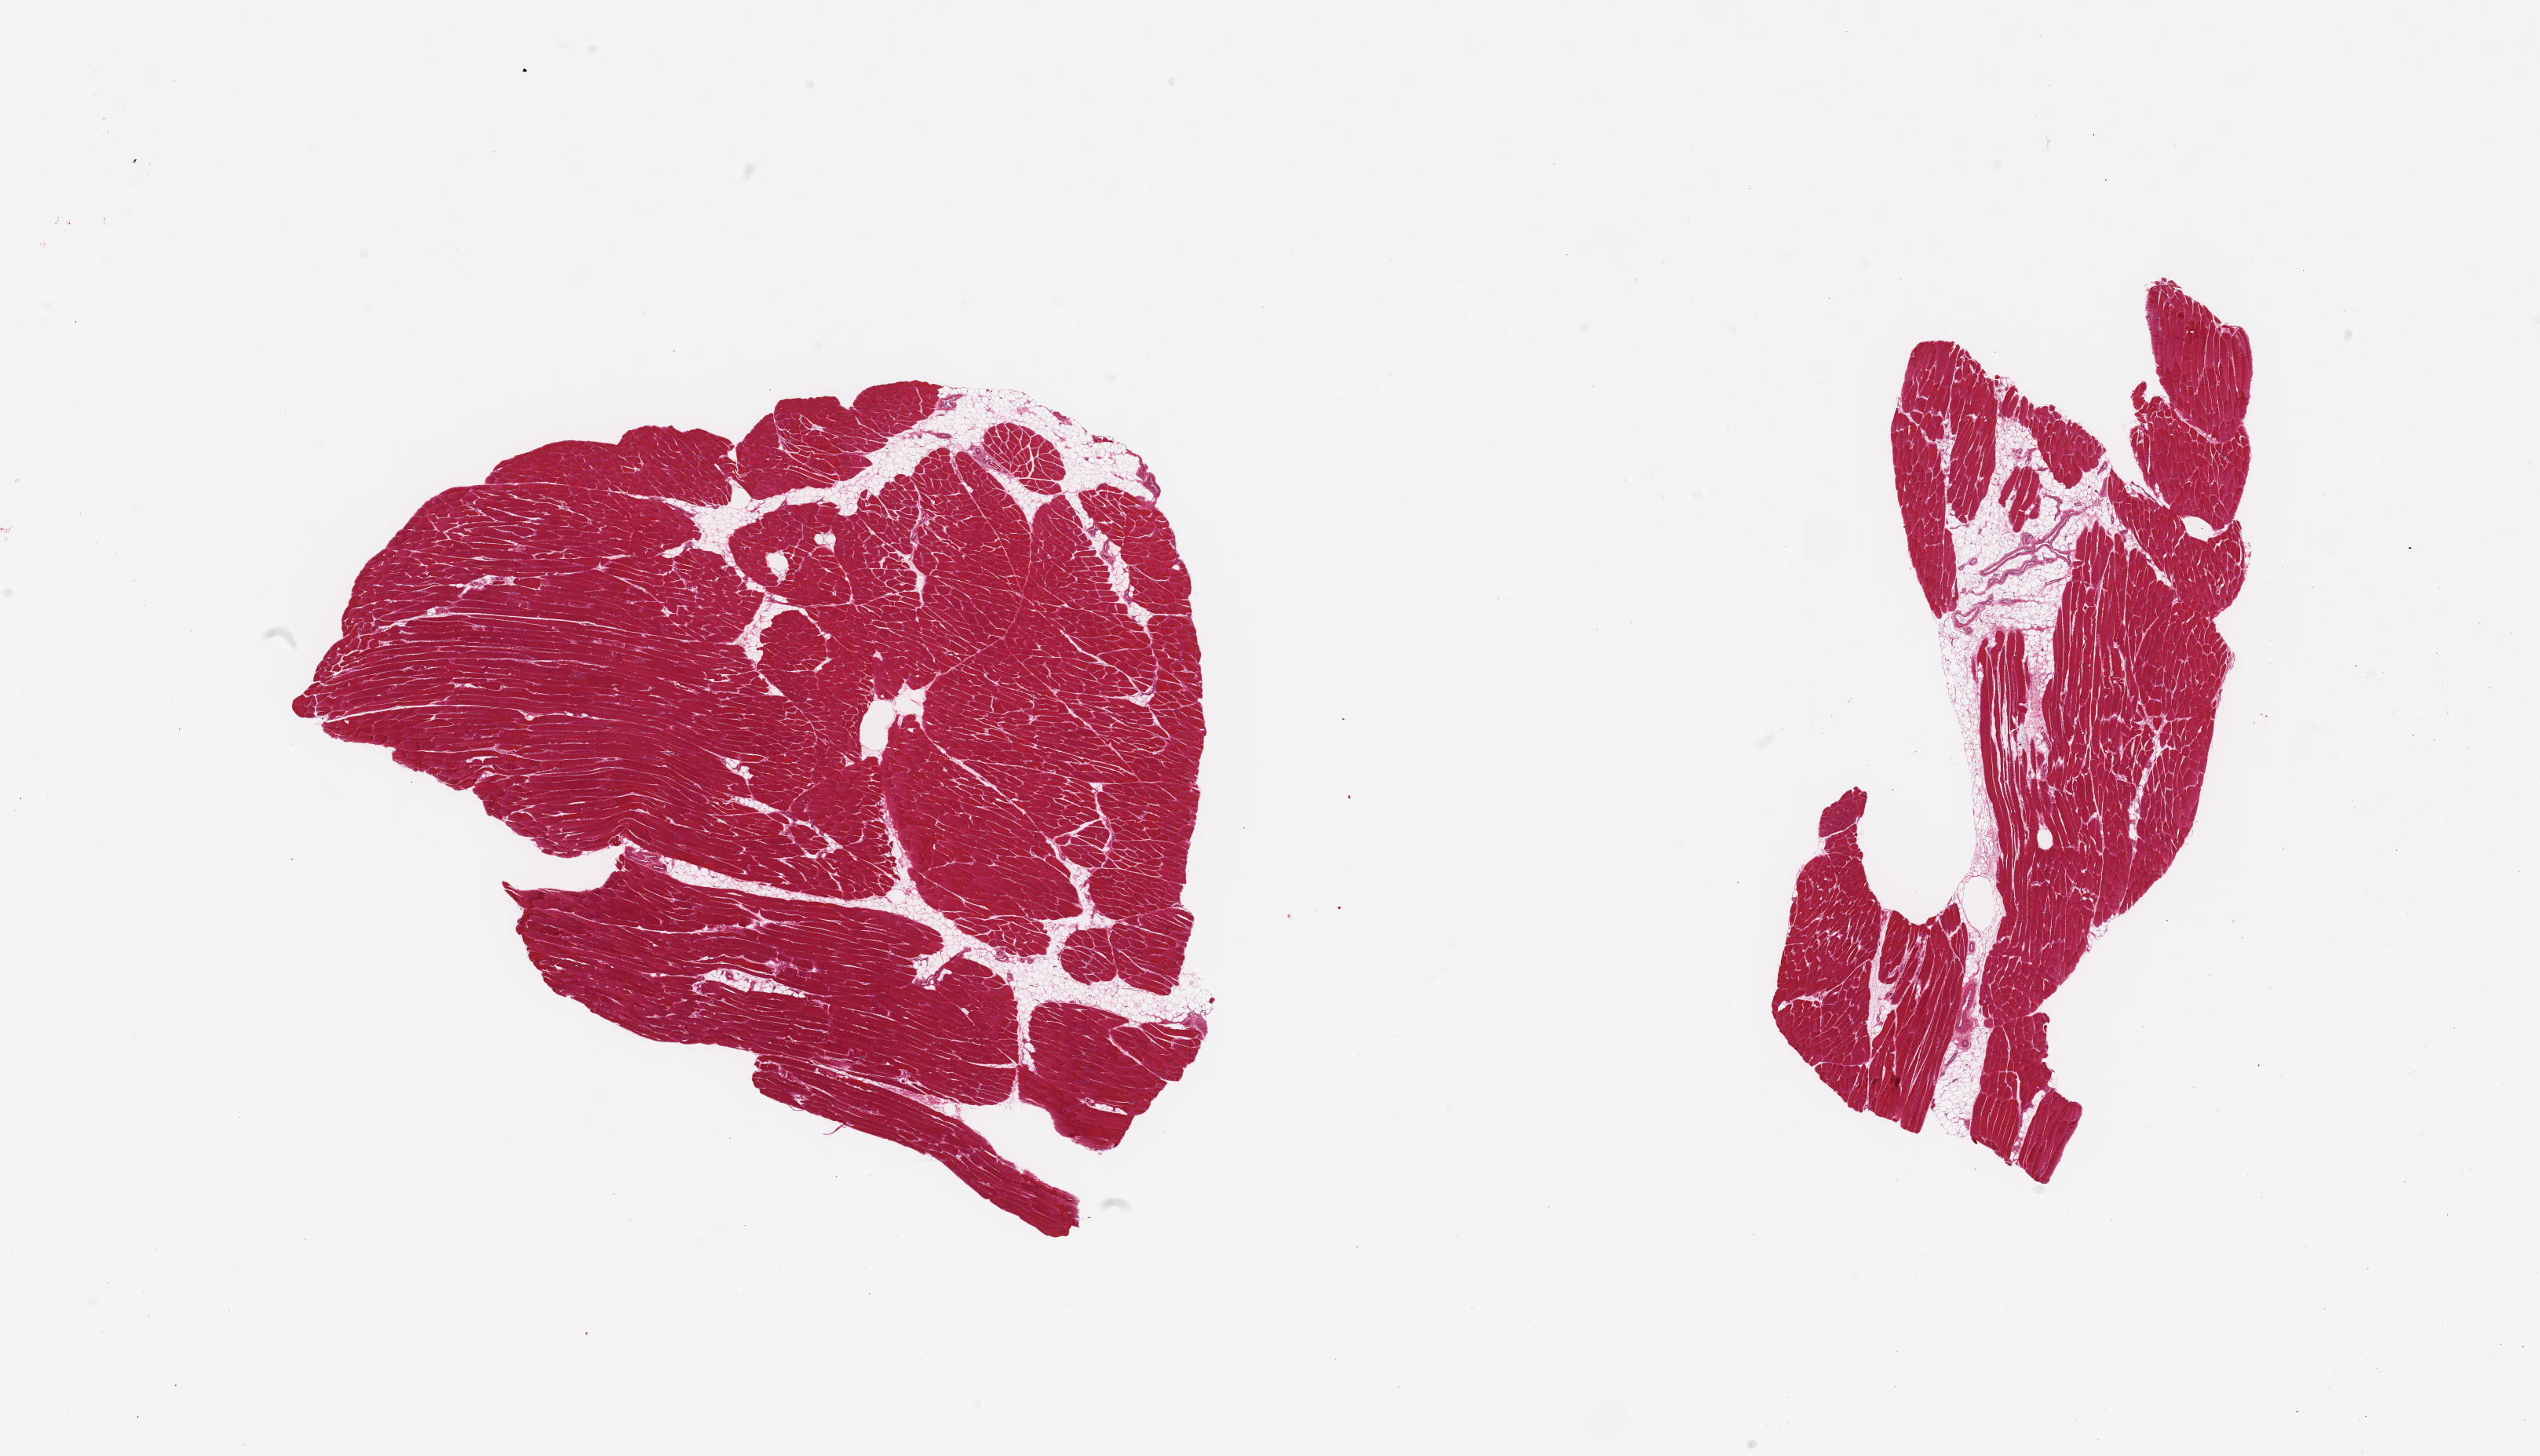
Whole-slide image, H&E stain — whole scanned area (about 25.6 x 14.7 mm) shown as a low-resolution overview; PAXgene-fixed paraffin-embedded (PFPE) section; sampled site (target tissue): skeletal muscle; tissue donor sample. Male donor.
Review note (as recorded): 2 pieces; 5% to 10% internal/external fat.